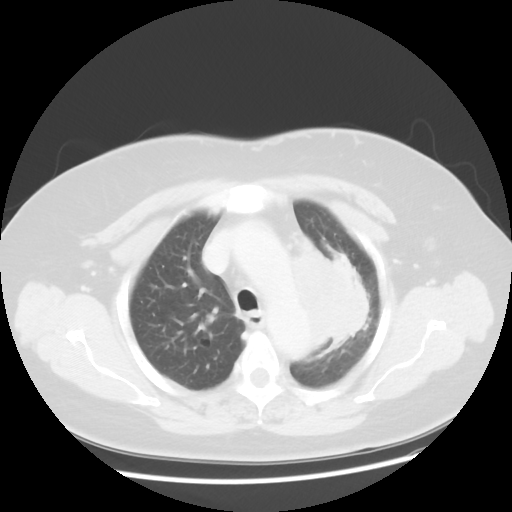
Chest CT, one axial slice. Reconstruction kernel STANDARD. 120 kVp. Lung window (W 1500 / L -600 HU). 5 mm slice thickness. 512 × 512 image matrix, field of view 374 × 374 mm. Female patient, age 58 years. Case-level facts recorded for this patient, not image findings: clinical TNM (as recorded): T4 N3 M0; histopathological grade: G3.
Outlined on this slice (bounding box drawn by a radiologist):
- lung tumour (recorded histology: small cell carcinoma): bounding box [x1, y1, x2, y2] px = [286, 231, 392, 356]